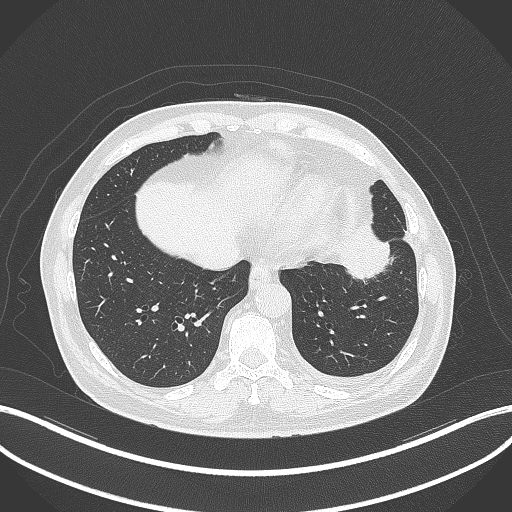
Chest CT, one axial slice; slice 94 of 230 in the series (ordered by position); lung window (W 1500 / L -600 HU); 1 mm slice thickness; 512 × 512 image matrix, field of view 400 × 400 mm. Patient: male, 68 years. From the clinical record (not read from this slice): clinical TNM (as recorded): T2b N0 M0.
Structures marked on this image (bounding box drawn by a radiologist):
- lung tumour (recorded histology: squamous cell carcinoma): bounding box <336,219,397,289> (left, top, right, bottom; pixels)